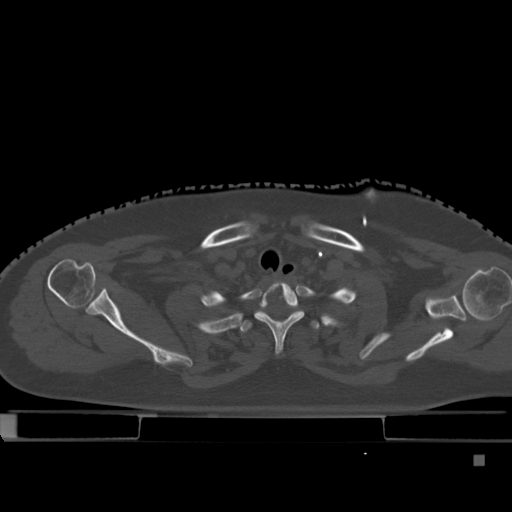
CT including the spine, one axial slice. Slice 368 of 495 in the series (ordered by position). Bone window (W 1800 / L 400 HU). 512 × 512 image matrix. Female patient, age 33 years. From the clinical record (not read from this slice): primary cancer: breast; vertebrae with lytic lesions (as recorded): T1.
Structures marked on this image (semi-automatic segmentation, software-assisted and operator-edited):
- T1 vertebra: box from (x=255, y=282) to (x=303, y=353) px
- T2 vertebra: (x=240, y=310)–(x=342, y=333)